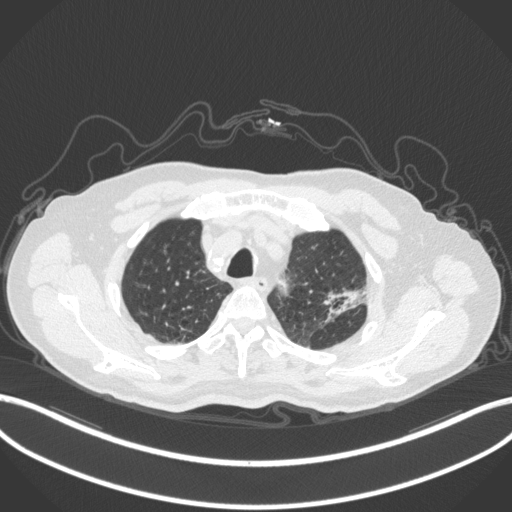
Chest CT, one axial slice. Slice 250 of 331 in the series (ordered by position). Reconstruction kernel B31f. 120 kVp. Lung window (W 1500 / L -600 HU). 1 mm slice thickness. 512 × 512 image matrix. Patient: male, 79 years. From the clinical record (not read from this slice): clinical TNM (as recorded): T2a N1 M1.
Outlined on this slice (rectangle marked by the reading radiologist):
- lung tumour (recorded histology: adenocarcinoma): bounding box (x1, y1, x2, y2) in pixels: (321, 282, 369, 320)